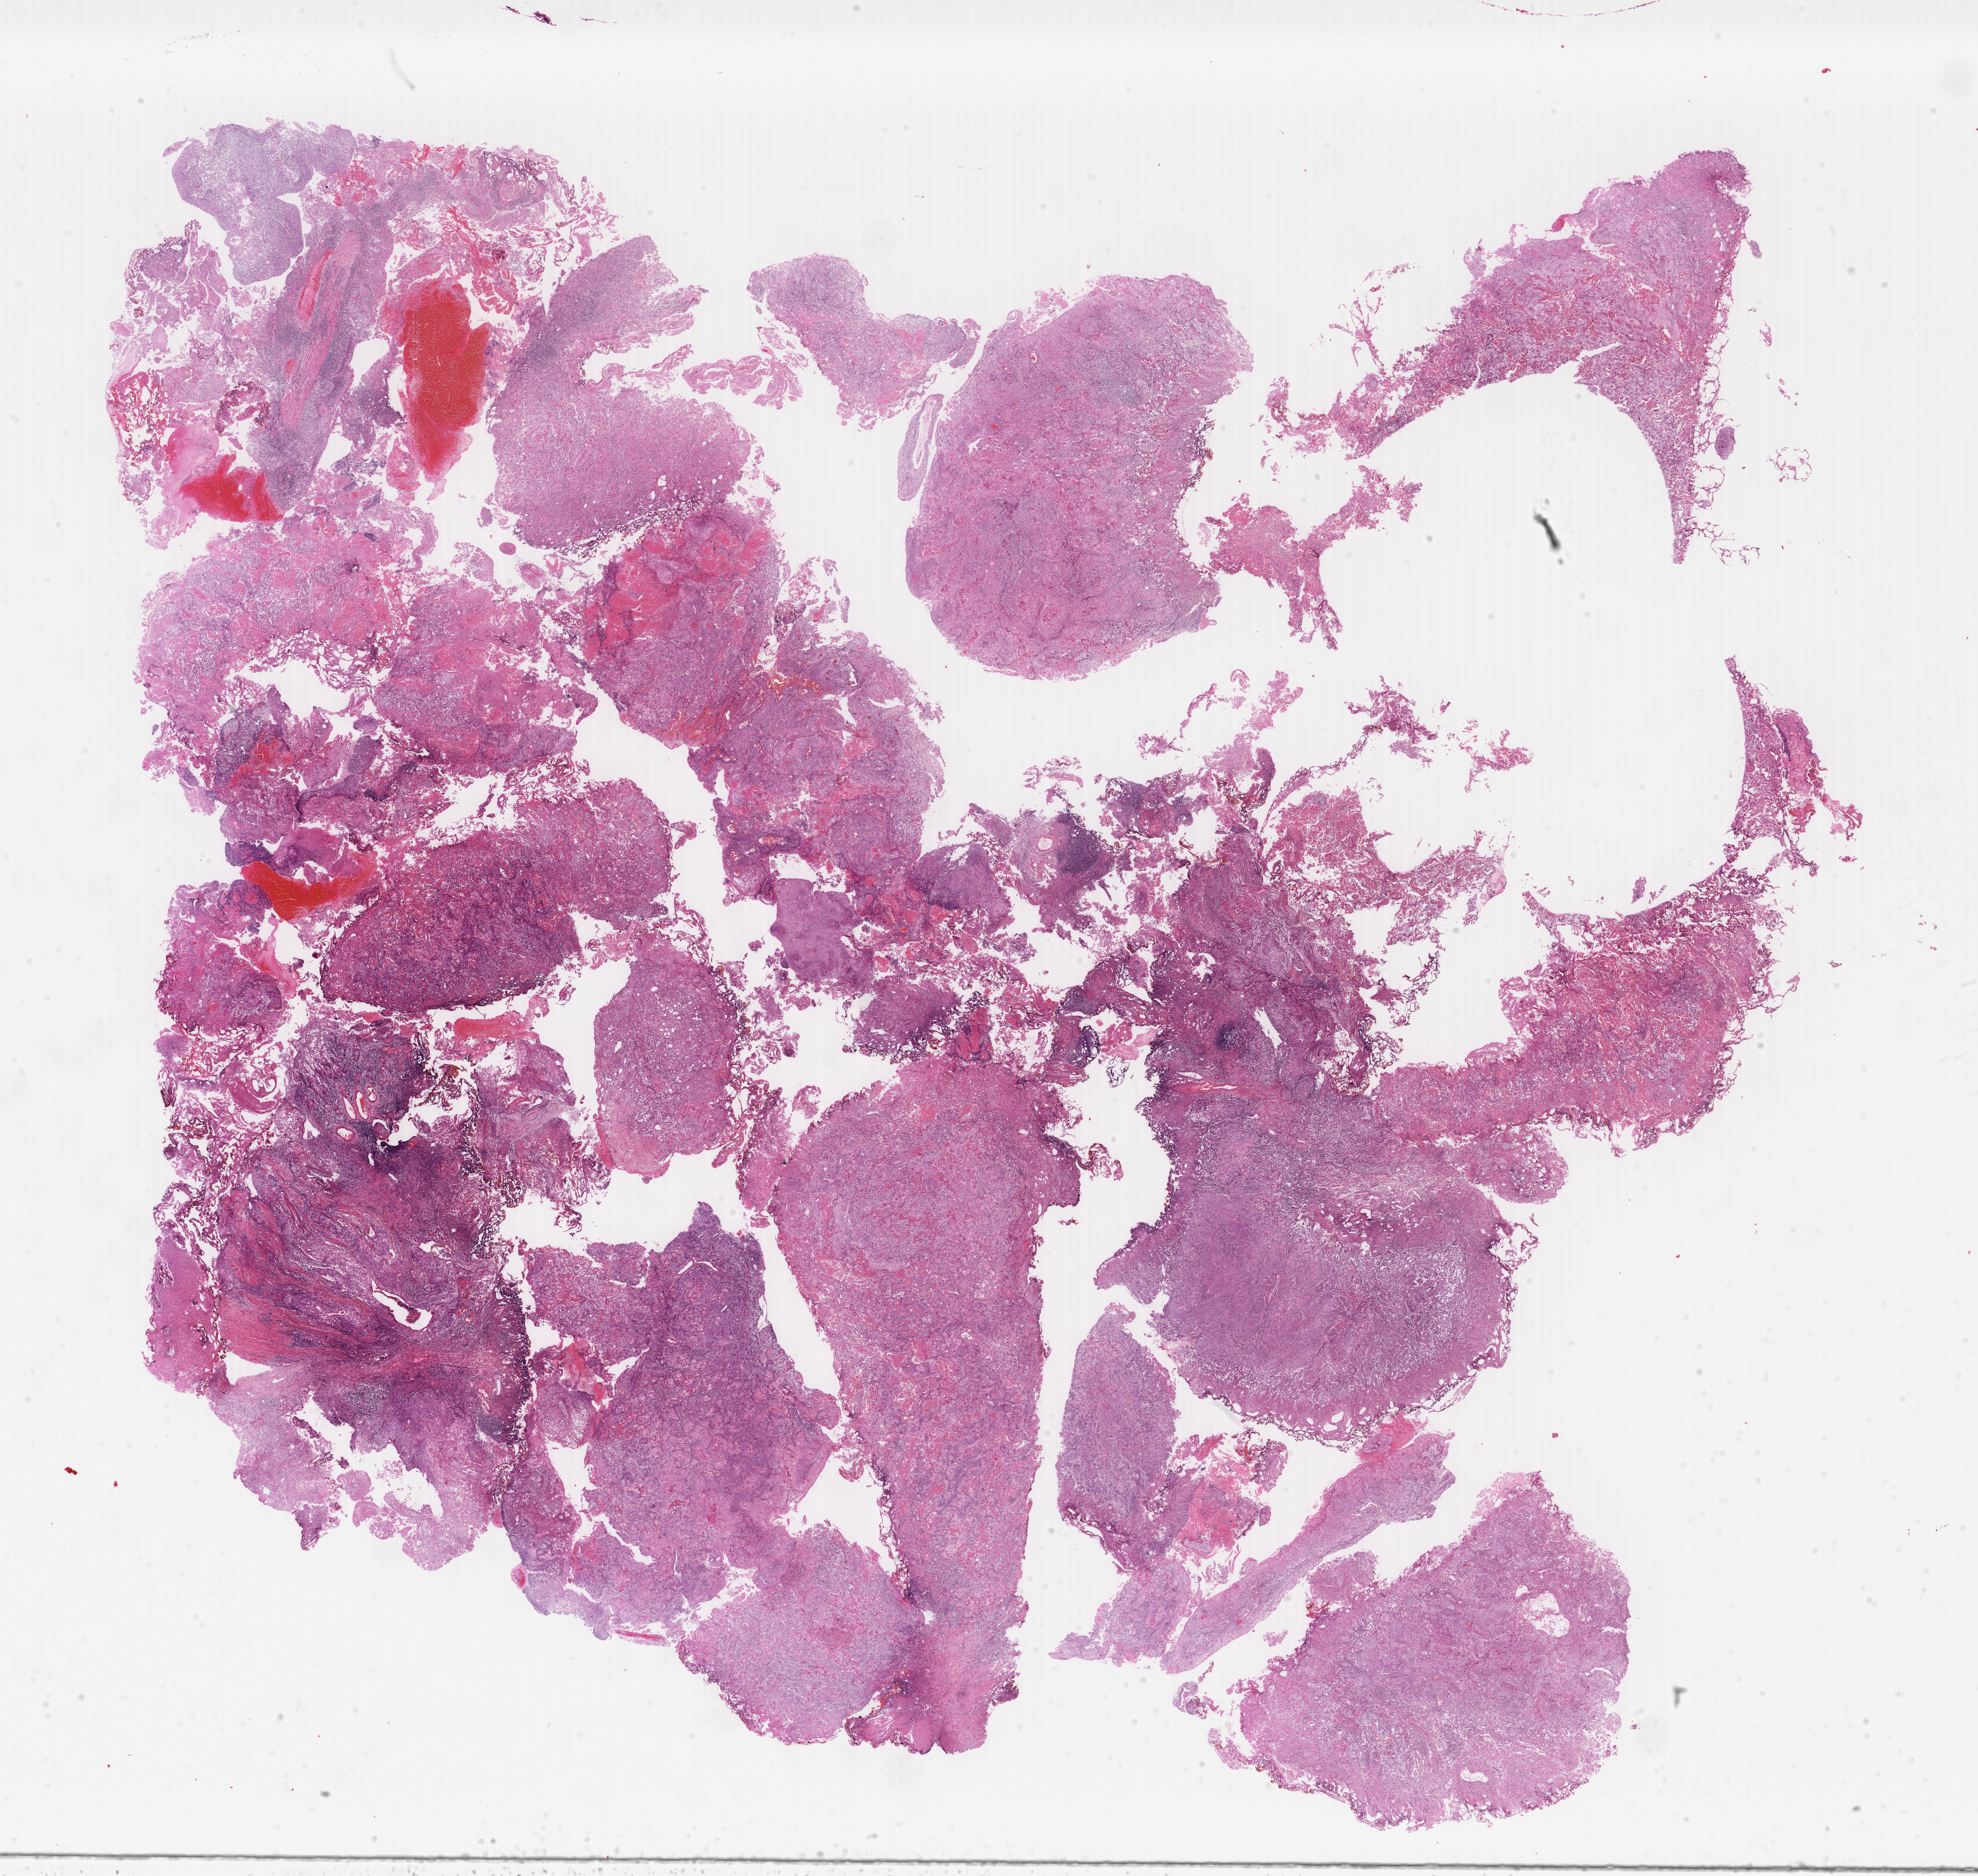
H&E whole-slide image, low-resolution overview of the scanned area, about 24.8 x 23.5 mm, formalin-fixed paraffin-embedded (FFPE) diagnostic section, sample: primary tumour, bladder. Female patient; age at initial diagnosis 56 years. Histologic grade: high grade.
Diagnosis: Transitional cell carcinoma. TNM: N0 M0. AJCC pathologic stage: II (6th edition).